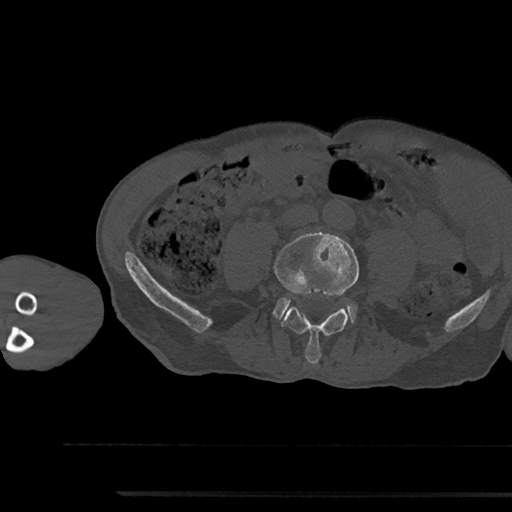
CT including the spine, one axial slice. Position 393 of 797 along the scan axis. Bone window (W 1800 / L 400 HU). 0.5 mm slice thickness. 512 × 512 image matrix, field of view 367 × 367 mm. Male patient, age 79 years. From the clinical record (not read from this slice): primary cancer: prostate.
Annotated regions visible in this slice (semi-automatically segmented with operator editing):
- L4 vertebra: bounding box <274,232,359,364> (left, top, right, bottom; pixels)
- L5 vertebra: <274,297,356,322>